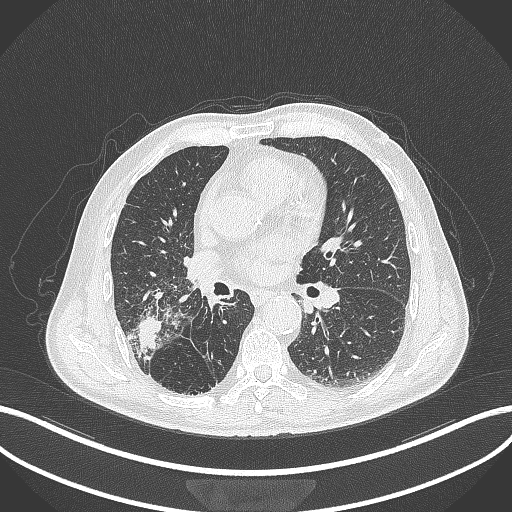
Chest CT, one axial slice. Slice 214 of 429 in the series (ordered by position). Reconstruction kernel B70f. 120 kVp. Lung window (W 1500 / L -600 HU). 1 mm slice thickness. 512 × 512 image matrix. Male patient, age 72 years. From the clinical record (not read from this slice): clinical TNM (as recorded): T3 N2 M0.
Annotated regions visible in this slice (bounding box drawn by a radiologist):
- lung tumour (recorded histology: adenocarcinoma): box from (x=130, y=312) to (x=168, y=356) px